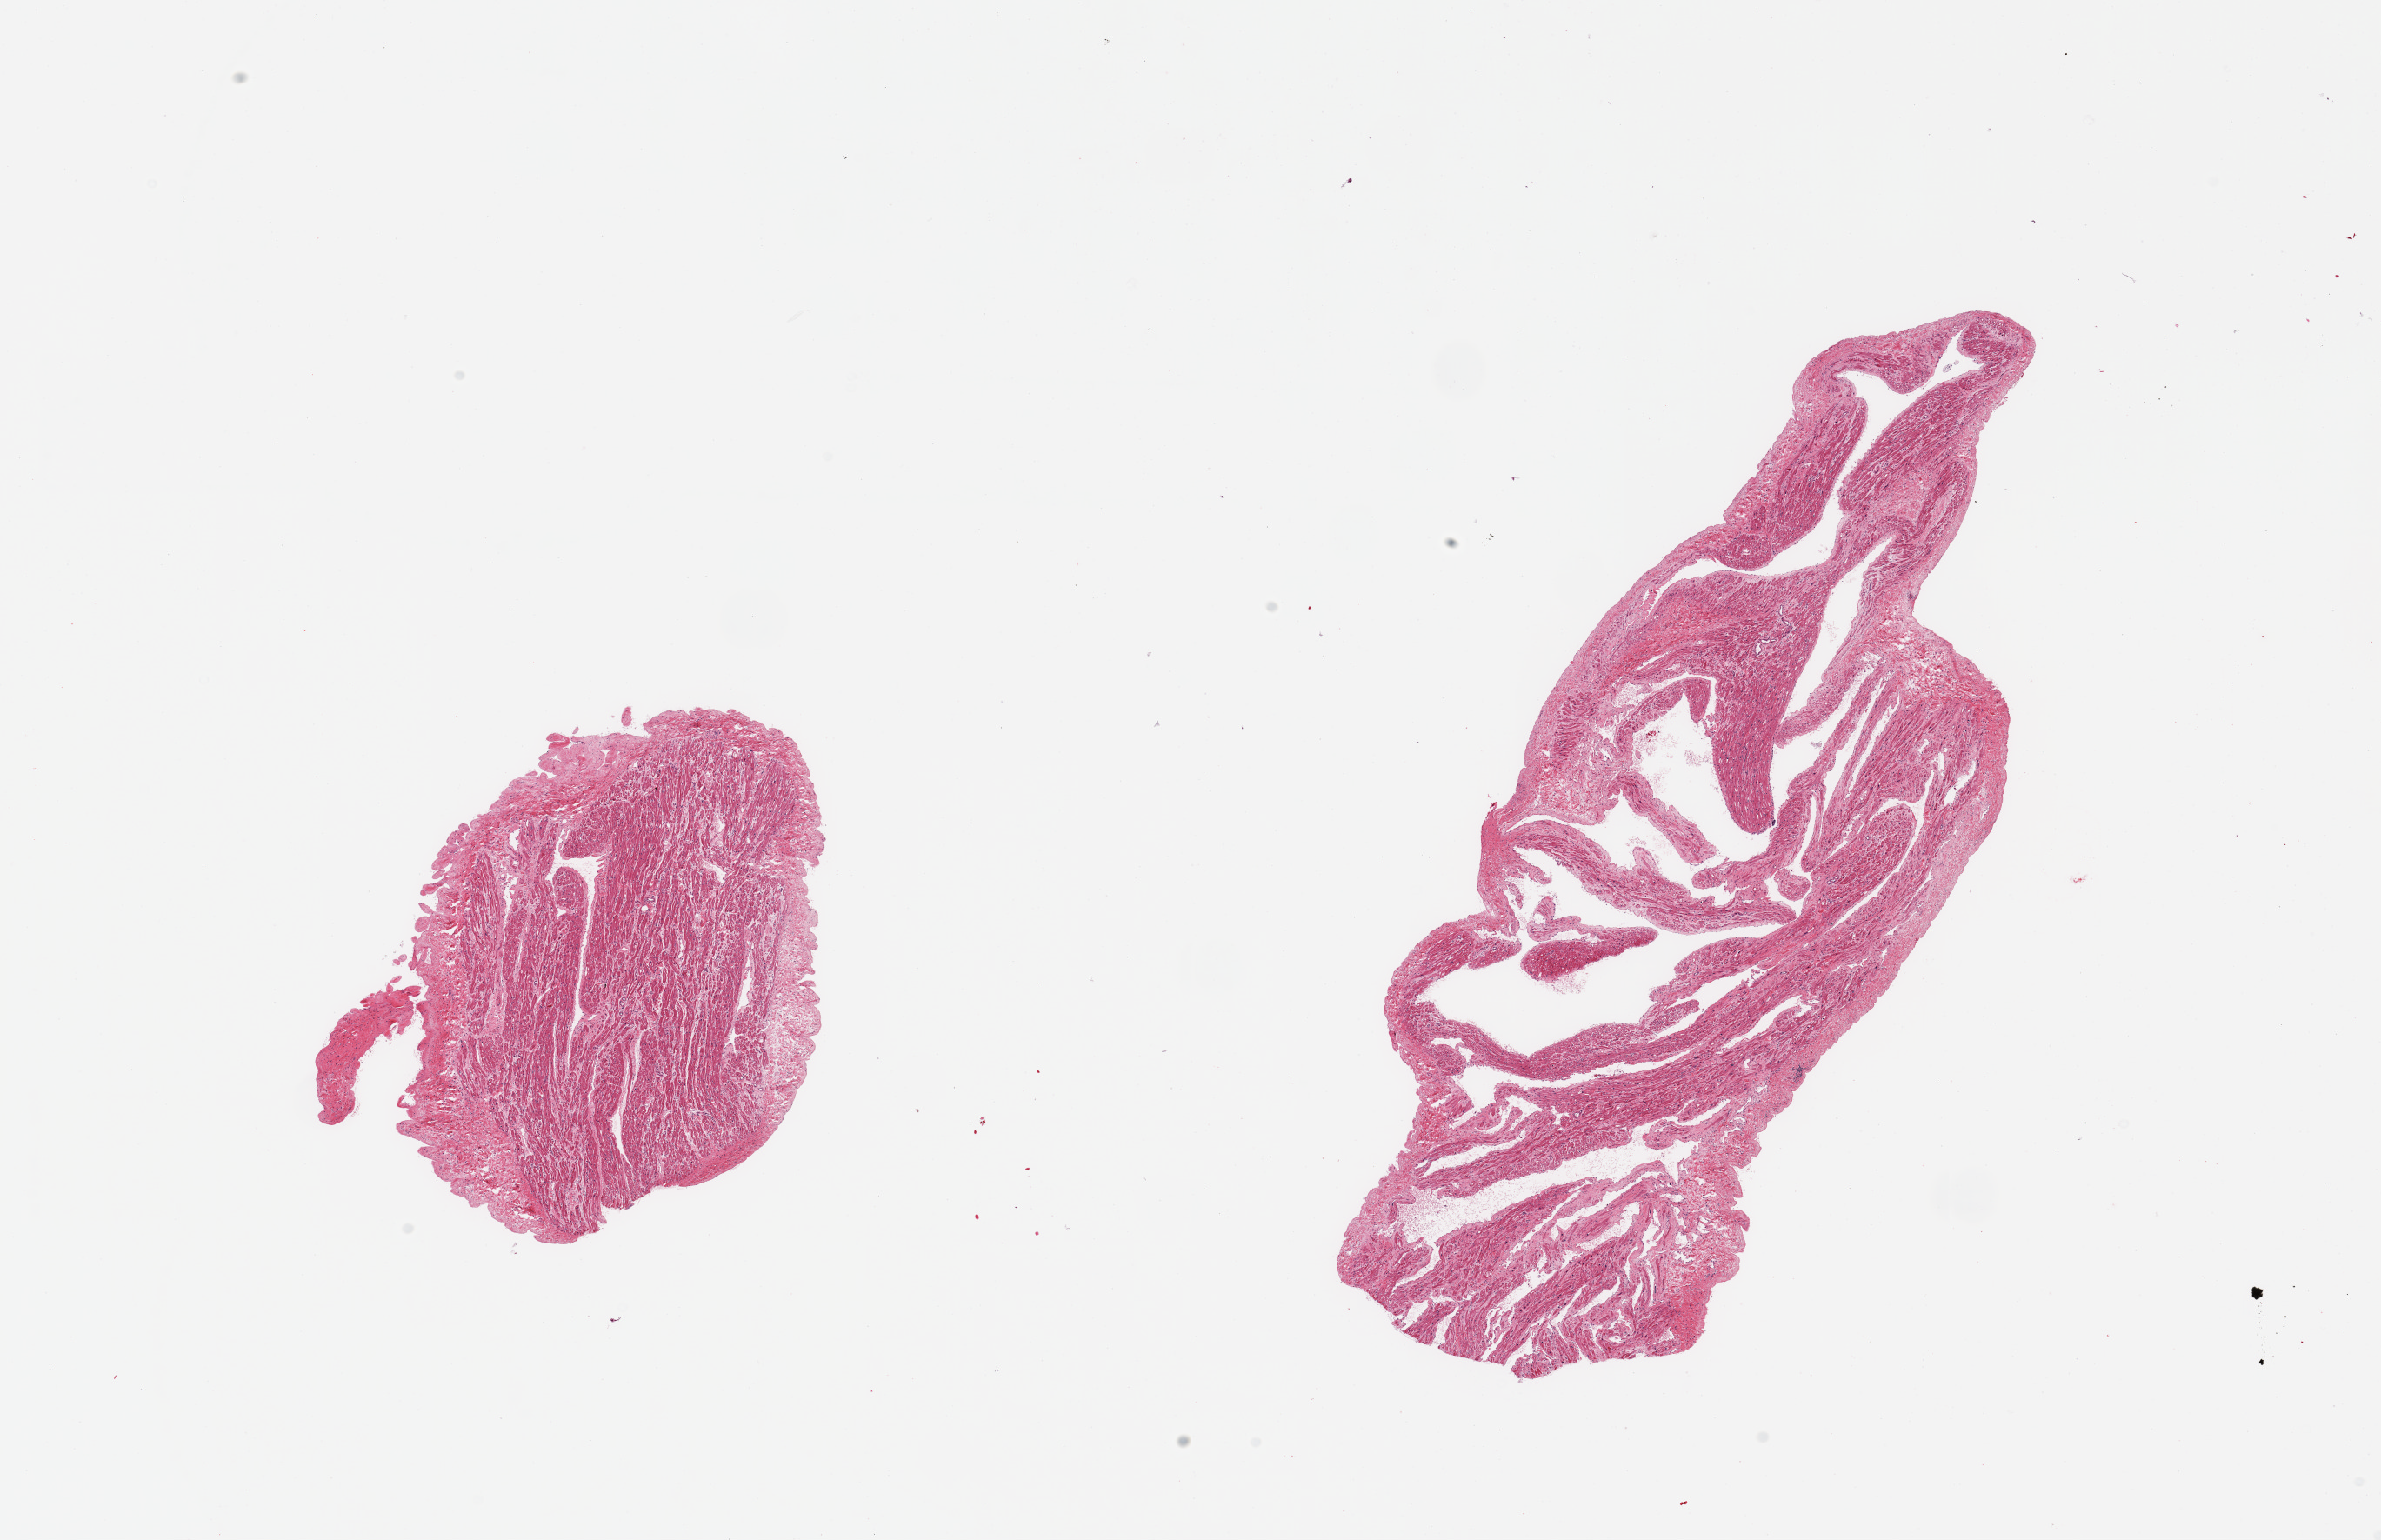
Digitized hematoxylin and eosin (H&E)-stained section — whole scanned area (about 21.7 x 14.0 mm, from a 20x scan) shown as a low-resolution overview, PAXgene-fixed paraffin-embedded (PFPE) section, sampled site (target tissue): auricular appendage, tissue donor sample.
Pathologist's review note for this sample: 2 pieces, no abnormalities.